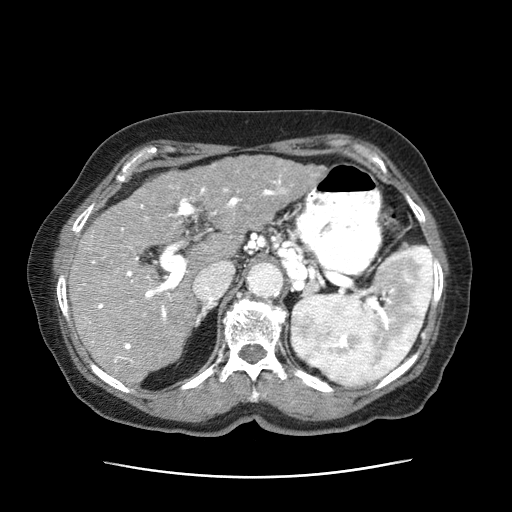
Contrast-enhanced abdominal CT (liver protocol), one axial slice. Position 40 of 63 along the scan axis. 120 kVp. Intravenous contrast given. Soft-tissue window (W 400 / L 40 HU). 2.5 mm slice thickness. 512 × 512 image matrix, field of view 360 × 360 mm. Patient: female, 79 years. Case-level facts recorded for this patient, not image findings: diagnosis: hepatocellular carcinoma (patient treated with transarterial chemoembolisation; whether this scan precedes or follows treatment is not stated here); TNM stage (as recorded): Stage-II; Child-Pugh class: B; tumour differentiation: well differentiated; tumour size: 5 cm.
Annotated regions visible in this slice (semi-automatic segmentation, software-assisted and operator-edited):
- abdominal aorta: bounding box [x1, y1, x2, y2] px = [247, 265, 283, 299]
- liver parenchyma outside the tumour (the mass and vessels are separate outlines, so this box may not span the whole liver): [70, 172, 248, 387]
- mass: [167, 154, 327, 234]
- liver vessels: [78, 175, 292, 363]